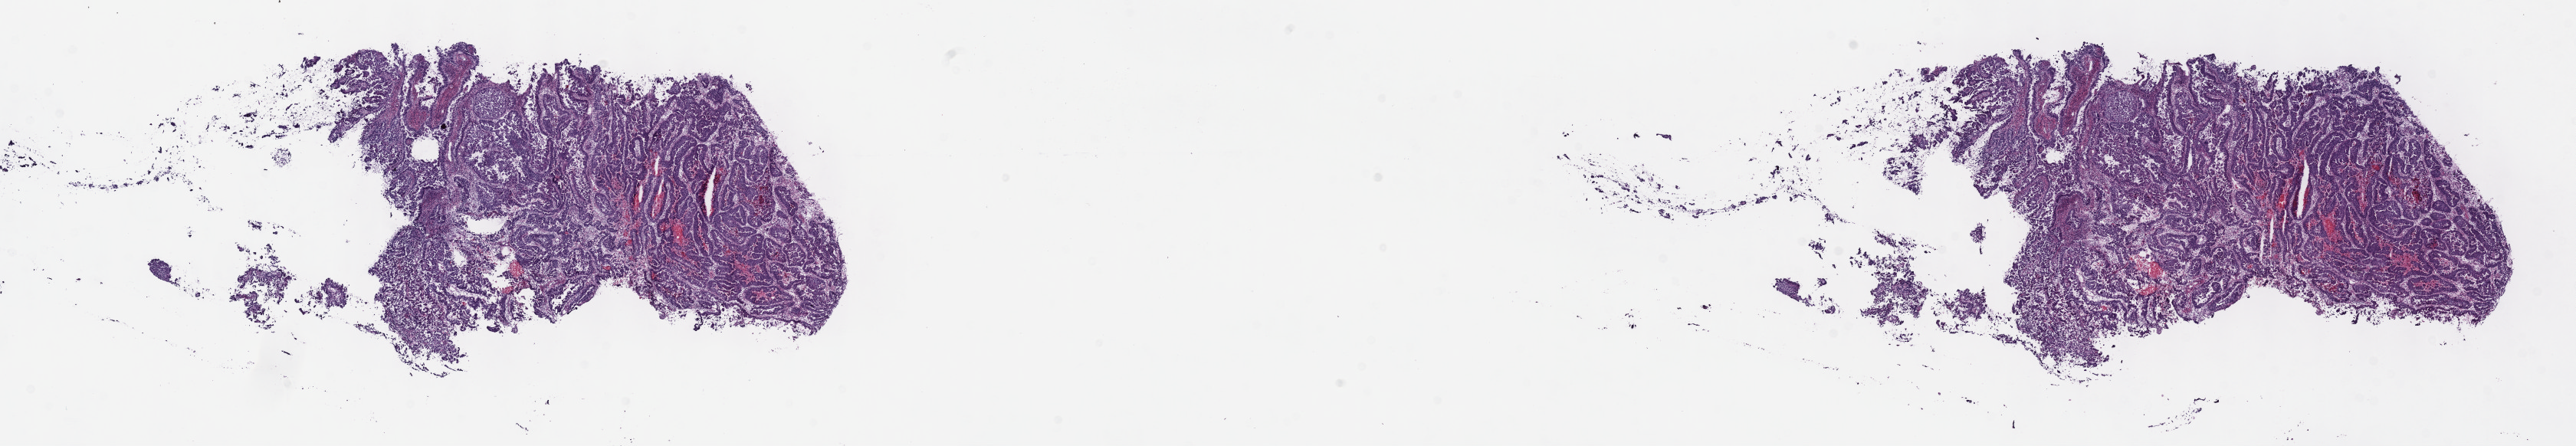
Digitized H&E tissue section (whole slide), whole scanned area (about 27.2 x 4.7 mm, acquisition: 40x scan) shown as a low-resolution overview, frozen section, primary tumour sample from the uterus. Female, age 85 years at initial diagnosis. Histologic grade: G3 (poorly differentiated). Slide review estimates, as recorded: tumour cells 70%, tumour nuclei 70%, normal cells 5%, stromal cells 20%, necrosis 5%. Inflammatory infiltration, as recorded: lymphocyte infiltration 1%, monocyte infiltration 1%, neutrophil infiltration 0%.
• histologic diagnosis: Serous cystadenocarcinoma, NOS (fundus uteri)
• FIGO stage: IIIA